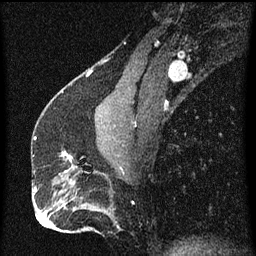
Breast MRI (dynamic contrast-enhanced), one sagittal slice; position 29 of 60 along the scan axis; dynamic contrast-enhanced series, image 2 of 3 at this slice position (ordered by acquisition); 1.5 T; TE 4.2 ms, TR 8 ms; 2 mm slice thickness; 256 × 256 image matrix, field of view 180 × 180 mm. Patient: female, 51 years.
Annotated regions visible in this slice (semi-automatically segmented with operator editing):
- analysis volume of interest (the breast-tissue region the enhancement analysis was run in; not a lesion): bounding box (x1, y1, x2, y2) in pixels: (60, 152, 91, 175)
- tumour enhancement mask (voxels above the 70 % enhancement threshold inside the analysis volume of interest): (62, 152, 73, 173)